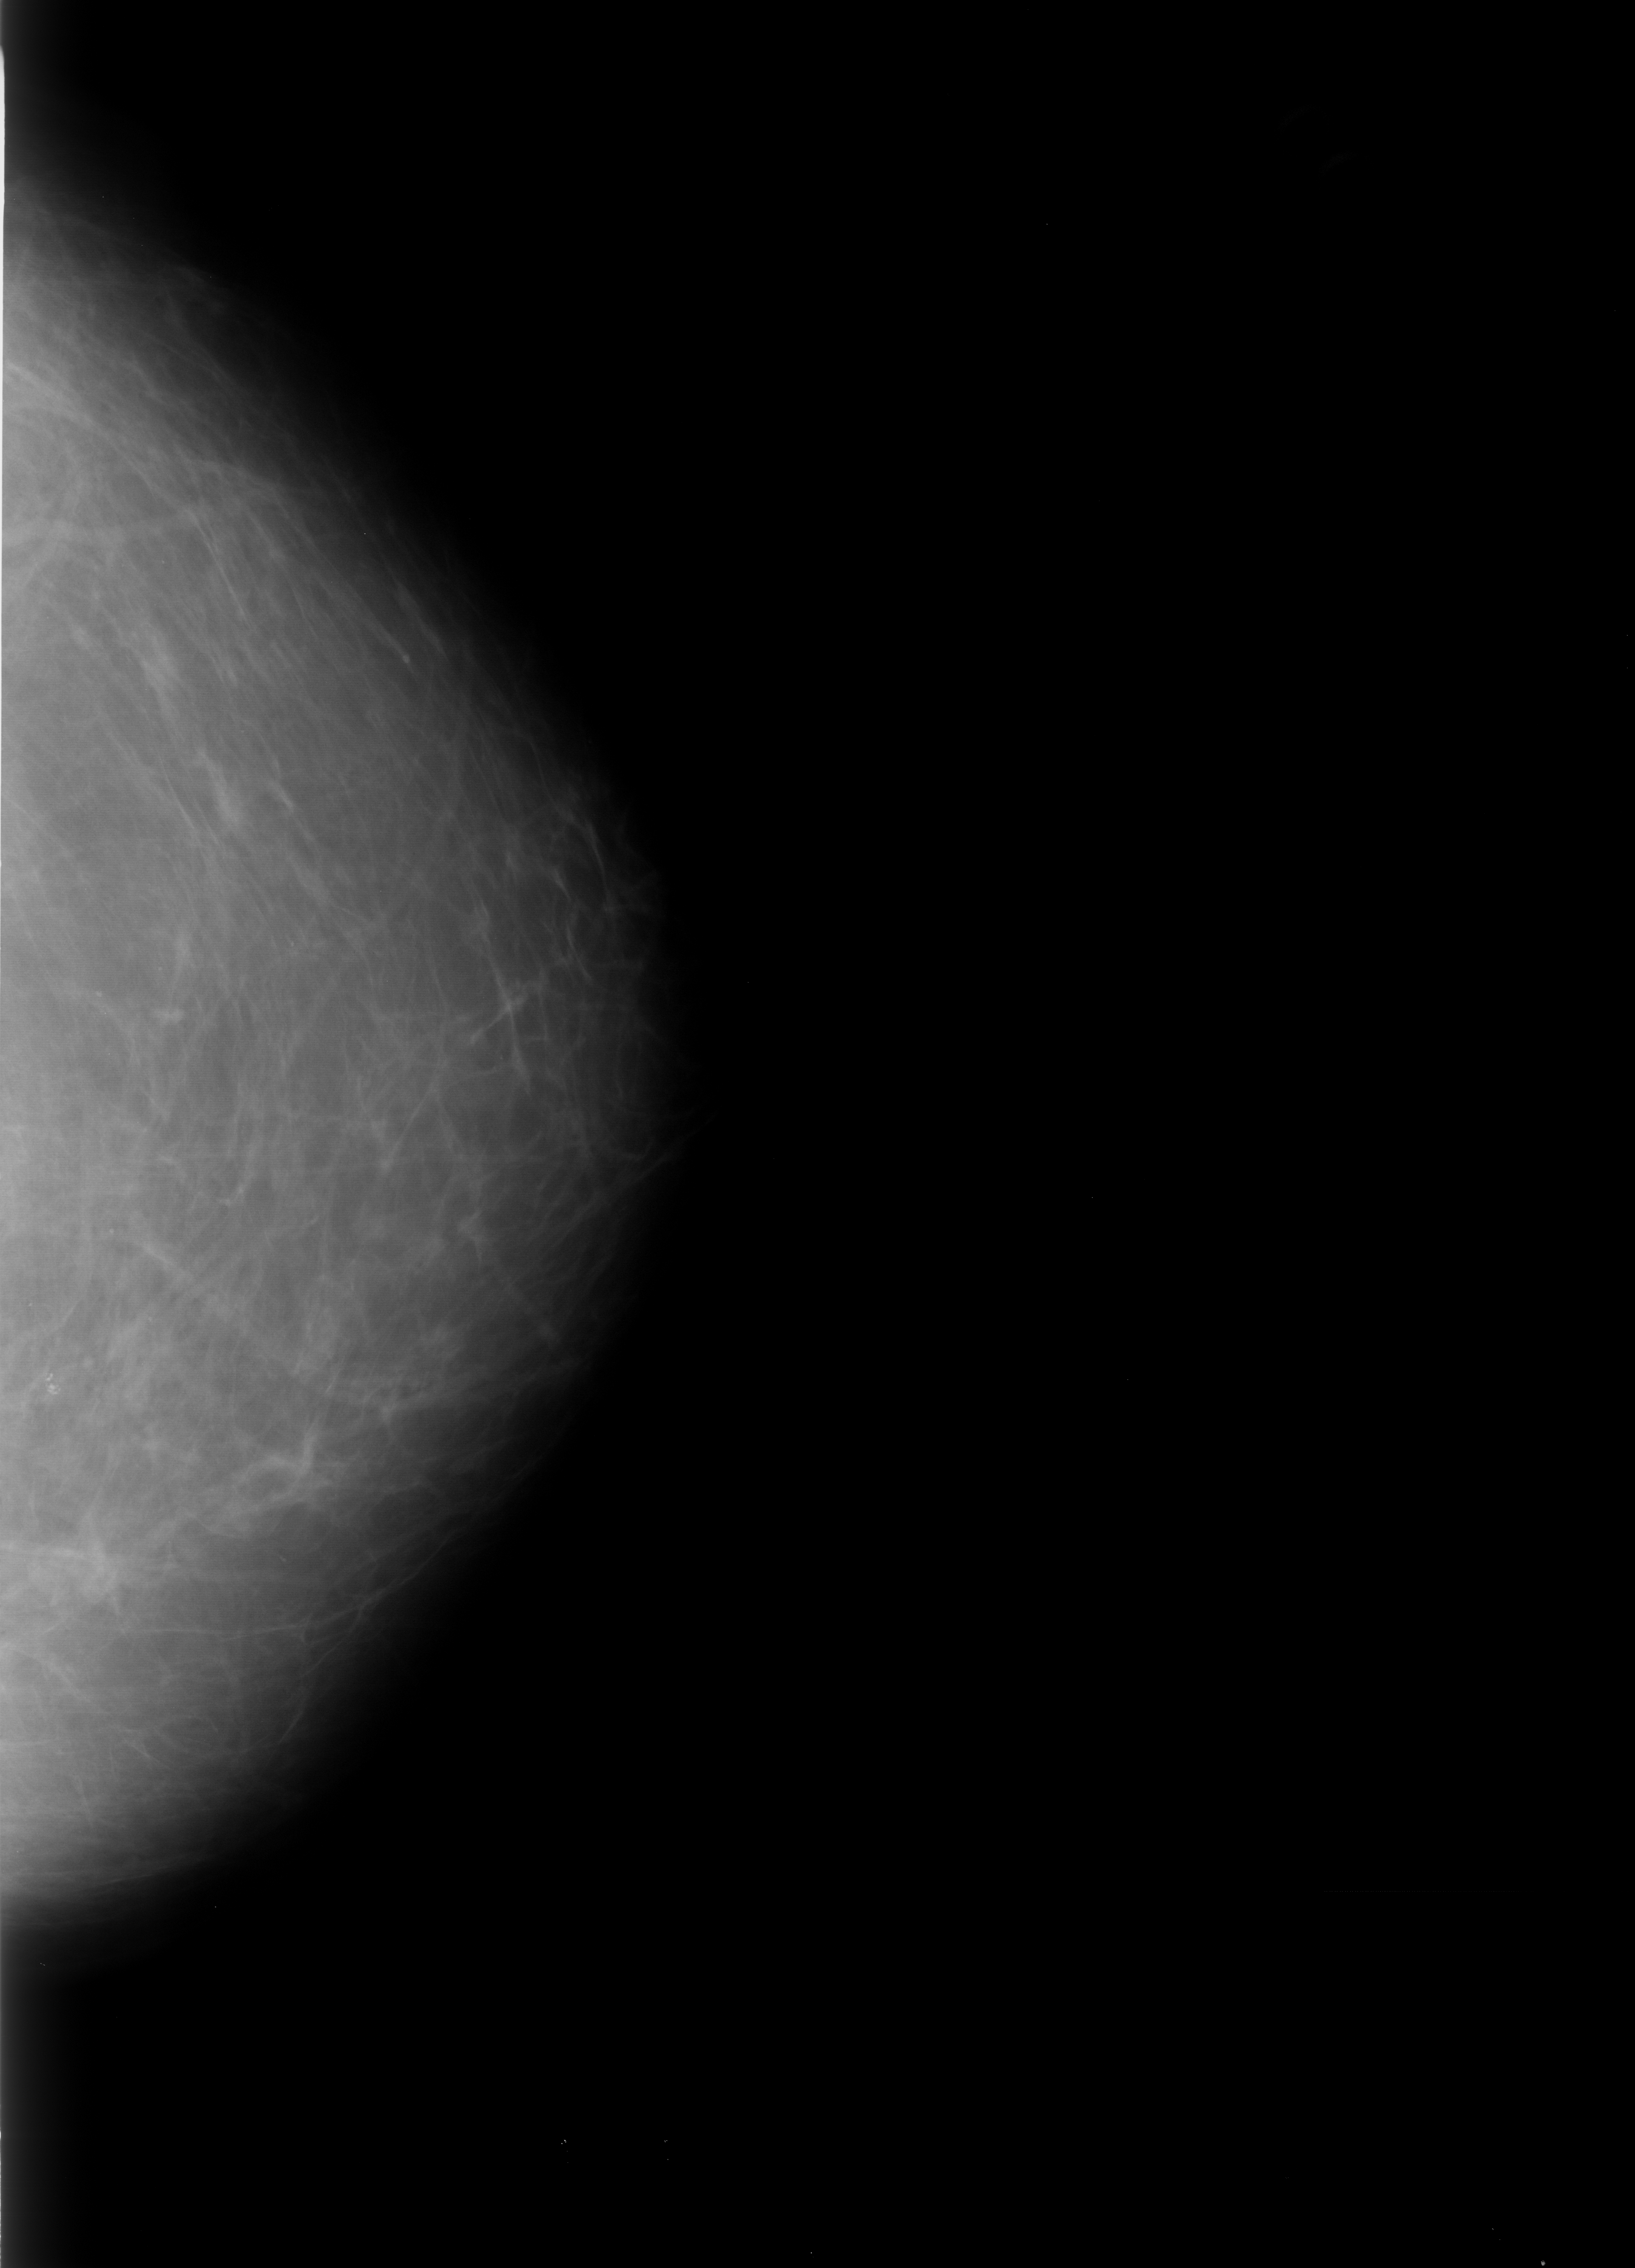
Scanned film-screen mammogram. Left breast. Craniocaudal (CC) view. BI-RADS breast density category 1 (scale 1–4). 1635 × 2268 image matrix.
Expert-marked regions of interest on this image (one box per marked abnormality):
- calcifications, morphology pleomorphic, distribution clustered; BI-RADS assessment category 4; pathology result (as recorded, not read from the image): benign: box from (x=25, y=1360) to (x=83, y=1421) px